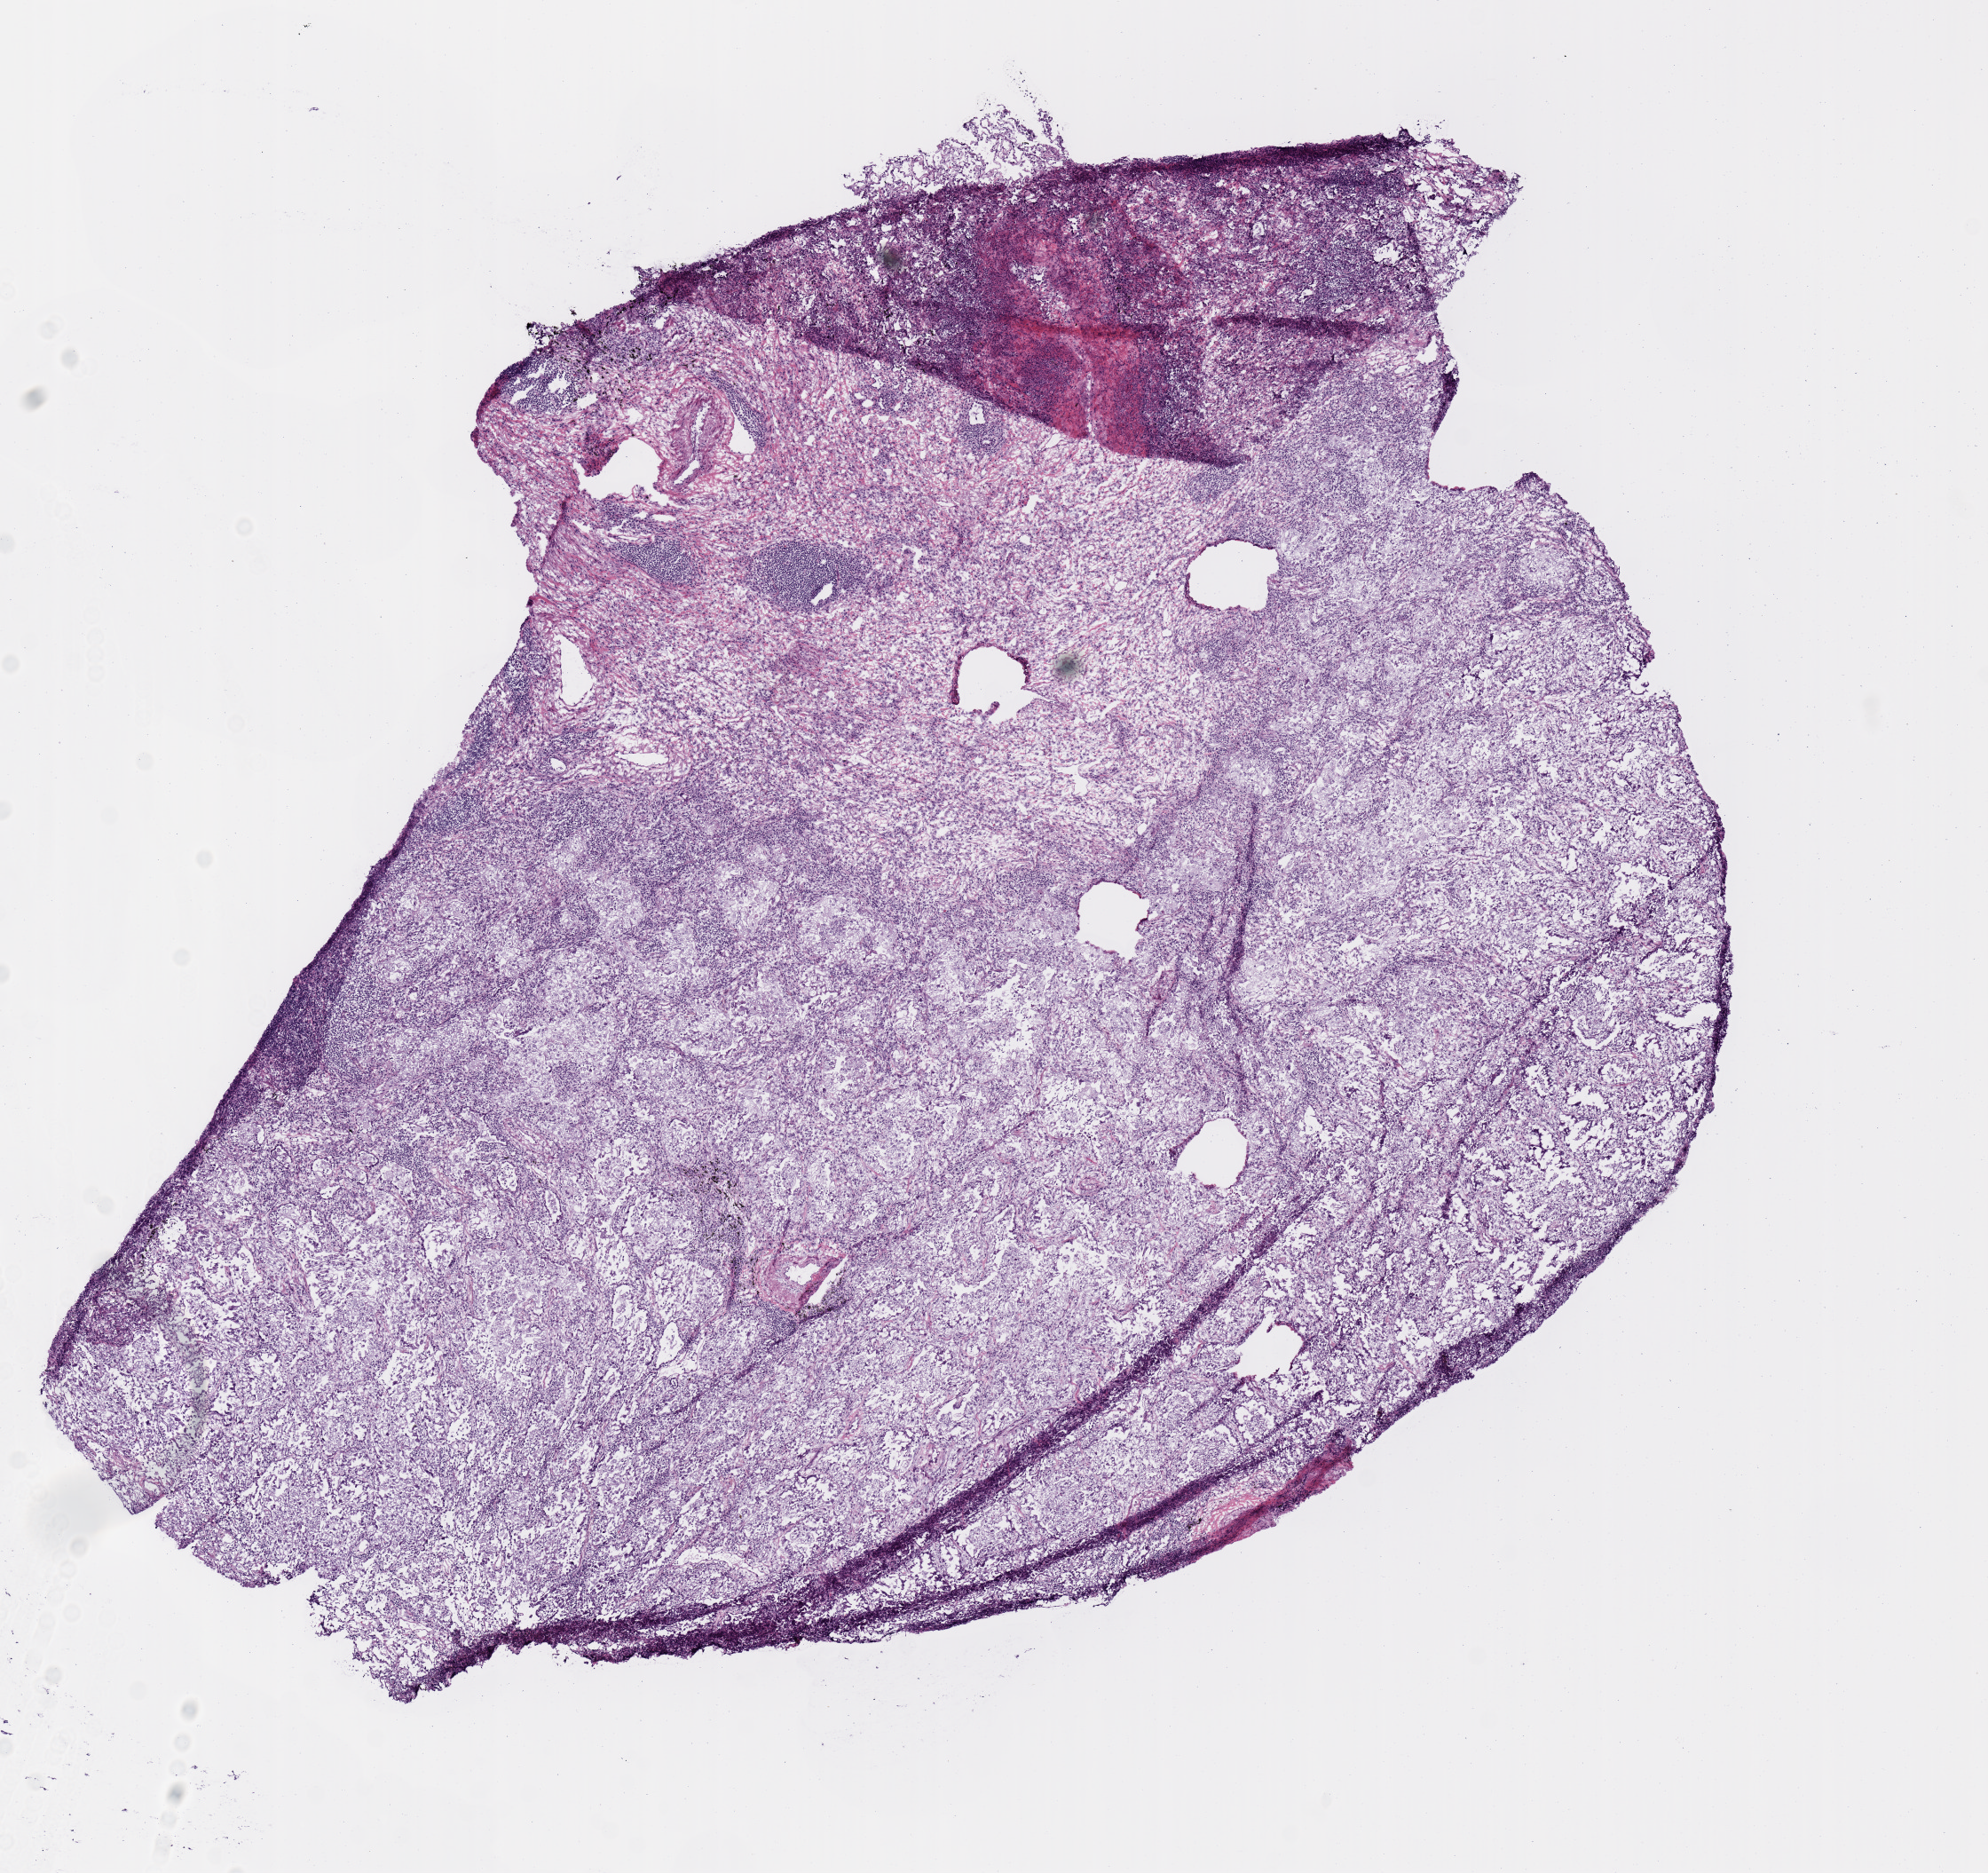
Whole-slide histology image, H&E — a low-resolution overview of the entire scanned area, about 8.9 x 8.3 mm (slide scanned at 20x), frozen section, primary tumour sample from the lung. Patient: female, age at initial diagnosis 70 years.
Pathologic diagnosis: Adenocarcinoma, NOS (middle lobe, lung).